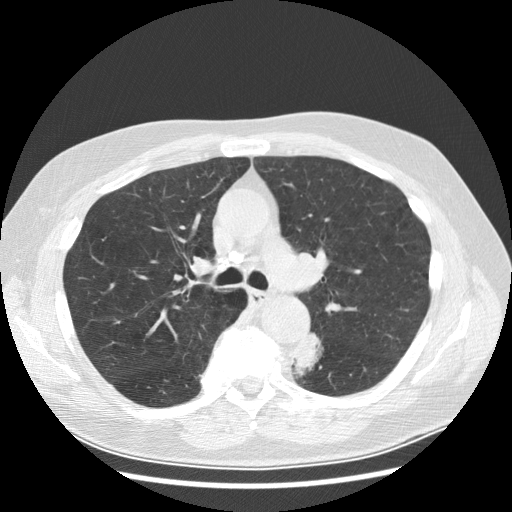
Low-dose screening chest CT, one axial slice. Slice 186 of 282 in the series (ordered by position). Reconstruction kernel STANDARD. 120 kVp. Lung window (W 1500 / L -600 HU). 2.5 mm slice thickness. 512 × 512 image matrix, field of view 370 × 370 mm.
Annotated regions visible in this slice (outlined manually by an expert reader):
- lesion 1 (tumor, lower lobe of left lung): box from (x=292, y=332) to (x=323, y=376) px